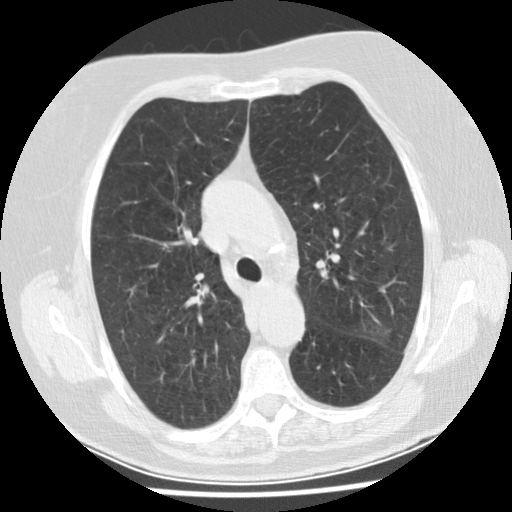
Chest CT (low-dose screening protocol), one axial image, baseline annual screen, lung window (W 1500 / L -600 HU), 120 kVp, slice 108 of 149 in the series, 512 × 512 image matrix. Female participant, aged 74 years at enrolment. Former smoker at enrolment.
Expert-annotated lung lesion, bounding box <342,303,411,357> (left, top, right, bottom; pixels). The screening reader recorded 2 non-calcified nodules or masses ≥4 mm on this exam (left upper lobe, left lower lobe); which of them this box marks is not recorded.